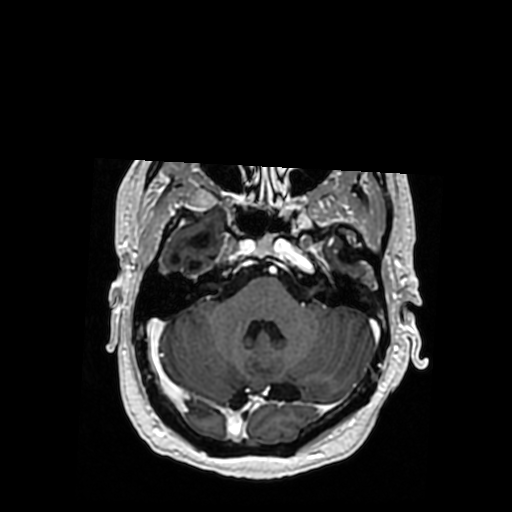
Brain MRI from a brain-tumour surgery series, one axial slice; slice 256 of 364 in the series (ordered by position); T1-weighted post-contrast; 512 × 512 image matrix, field of view 260 × 260 mm. From the clinical record (not read from this slice): histopathology: Oligodendroglioma; WHO grade: 3; IDH mutation: yes; tumour location: Right Posterior Temporal Inferior Parietal.
Outlined on this slice (outlined manually by an expert reader):
- previous resection cavity: bounding box [x1, y1, x2, y2] px = [171, 234, 210, 272]